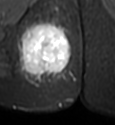
MRI of an extremity soft-tissue mass, one axial slice. Position 21 of 49 along the scan axis. STIR. MR volume resampled by the dataset authors to the PET/CT grid (not the native acquisition matrix). 3.27 mm slice thickness. 115 × 125 image matrix, field of view 112 × 122 mm. Female patient. Case-level facts recorded for this patient, not image findings: histological type: epithelioid sarcoma; grade: intermediate; site of the primary tumour: right buttock.
Annotated regions visible in this slice (expert contour drawn on MRI and transferred to this co-registered scan by the dataset authors):
- gross tumour volume including surrounding oedema: bounding box <15,18,71,83> (left, top, right, bottom; pixels)
- gross tumour volume (mass): <20,23,71,76>